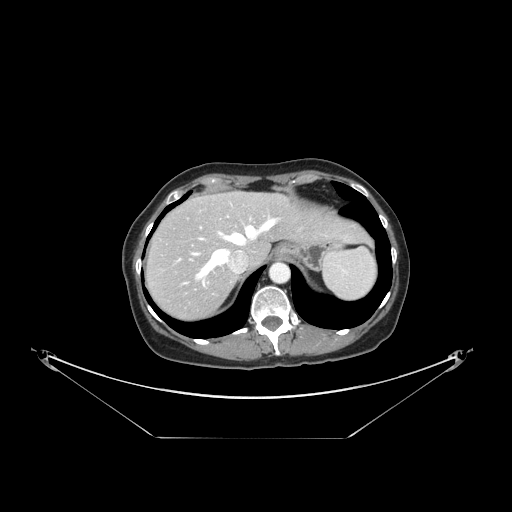
Contrast-enhanced abdominal CT, one axial slice; position 121 of 148 along the scan axis; reconstruction kernel STANDARD; intravenous contrast given; soft-tissue window (W 400 / L 40 HU); 2.5 mm slice thickness; 512 × 512 image matrix. Female patient, age 73 years. From the clinical record (not read from this slice): diagnosis: colorectal cancer liver metastases, imaged before liver resection; multiple liver metastases: no; largest metastasis: 1 cm; disease in both lobes: no.
Outlined on this slice (manually delineated by an expert):
- hepatic veins: bounding box [x1, y1, x2, y2] px = [195, 218, 279, 283]
- liver: [148, 193, 366, 318]
- planned liver remnant (the part of the liver to remain after resection): [173, 193, 366, 264]
- portal vein (with intrahepatic branches): [179, 227, 201, 260]